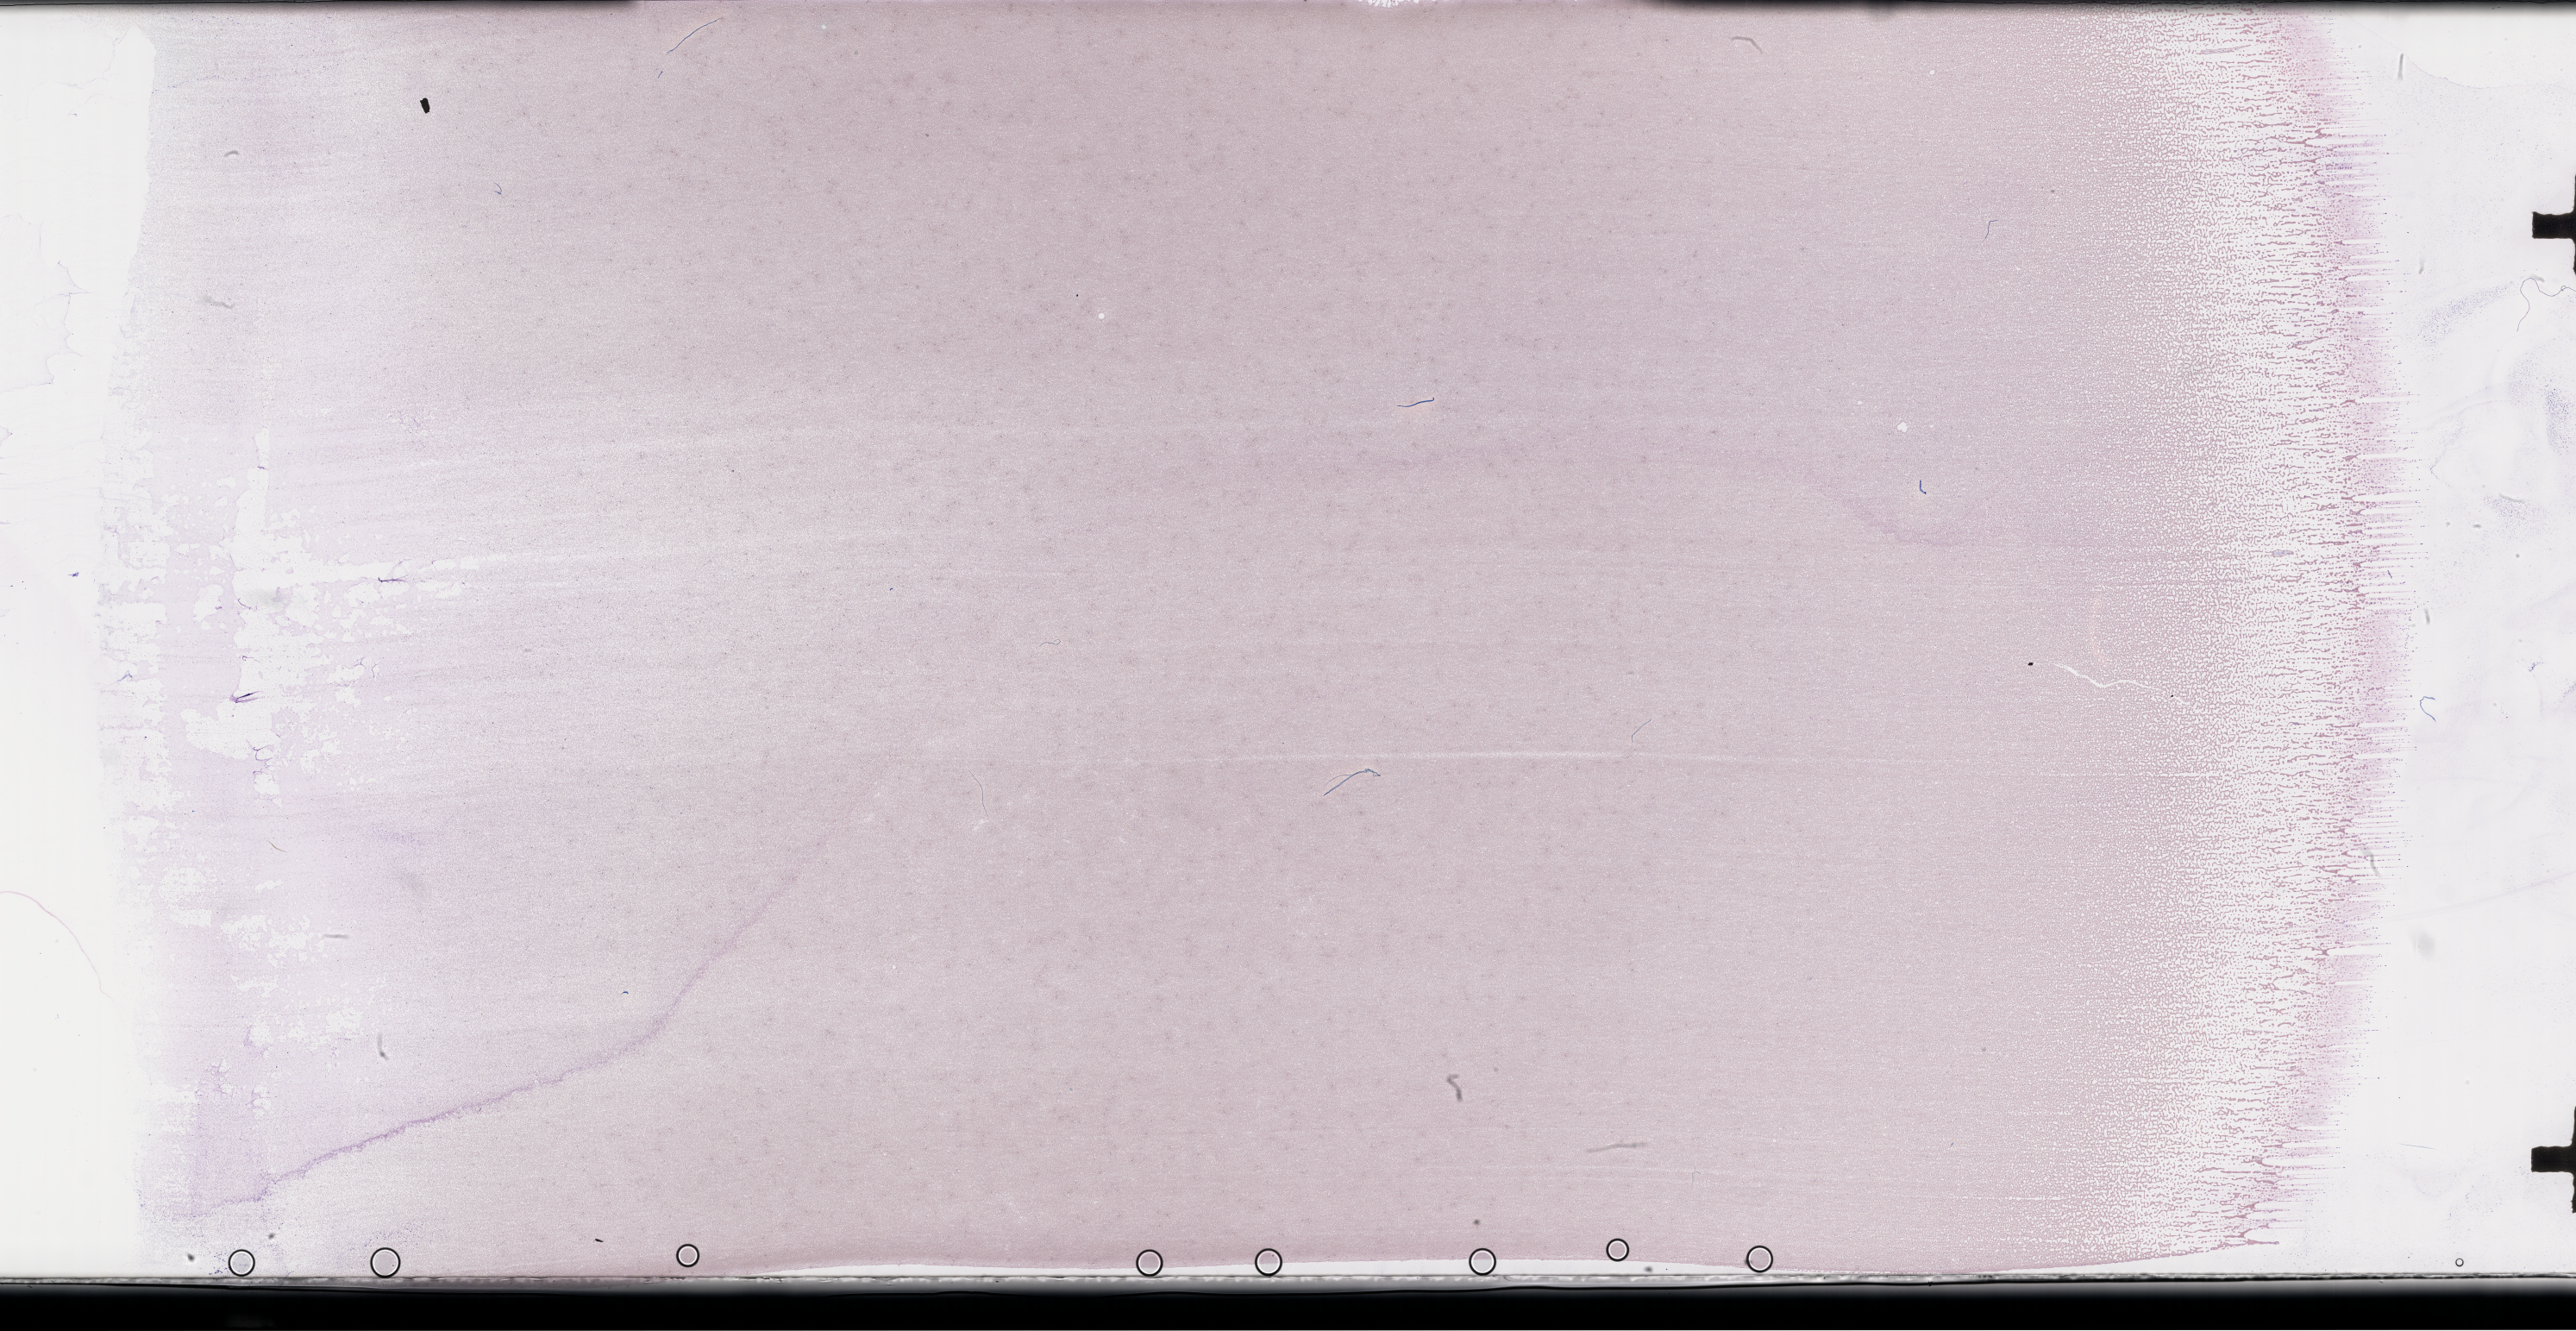
Wright-Giemsa-stained whole blood smear, whole-slide image, a low-resolution overview of the entire scanned area, about 48.2 x 24.9 mm. Patient: male.
From a patient with: Plasma Cell Myeloma.